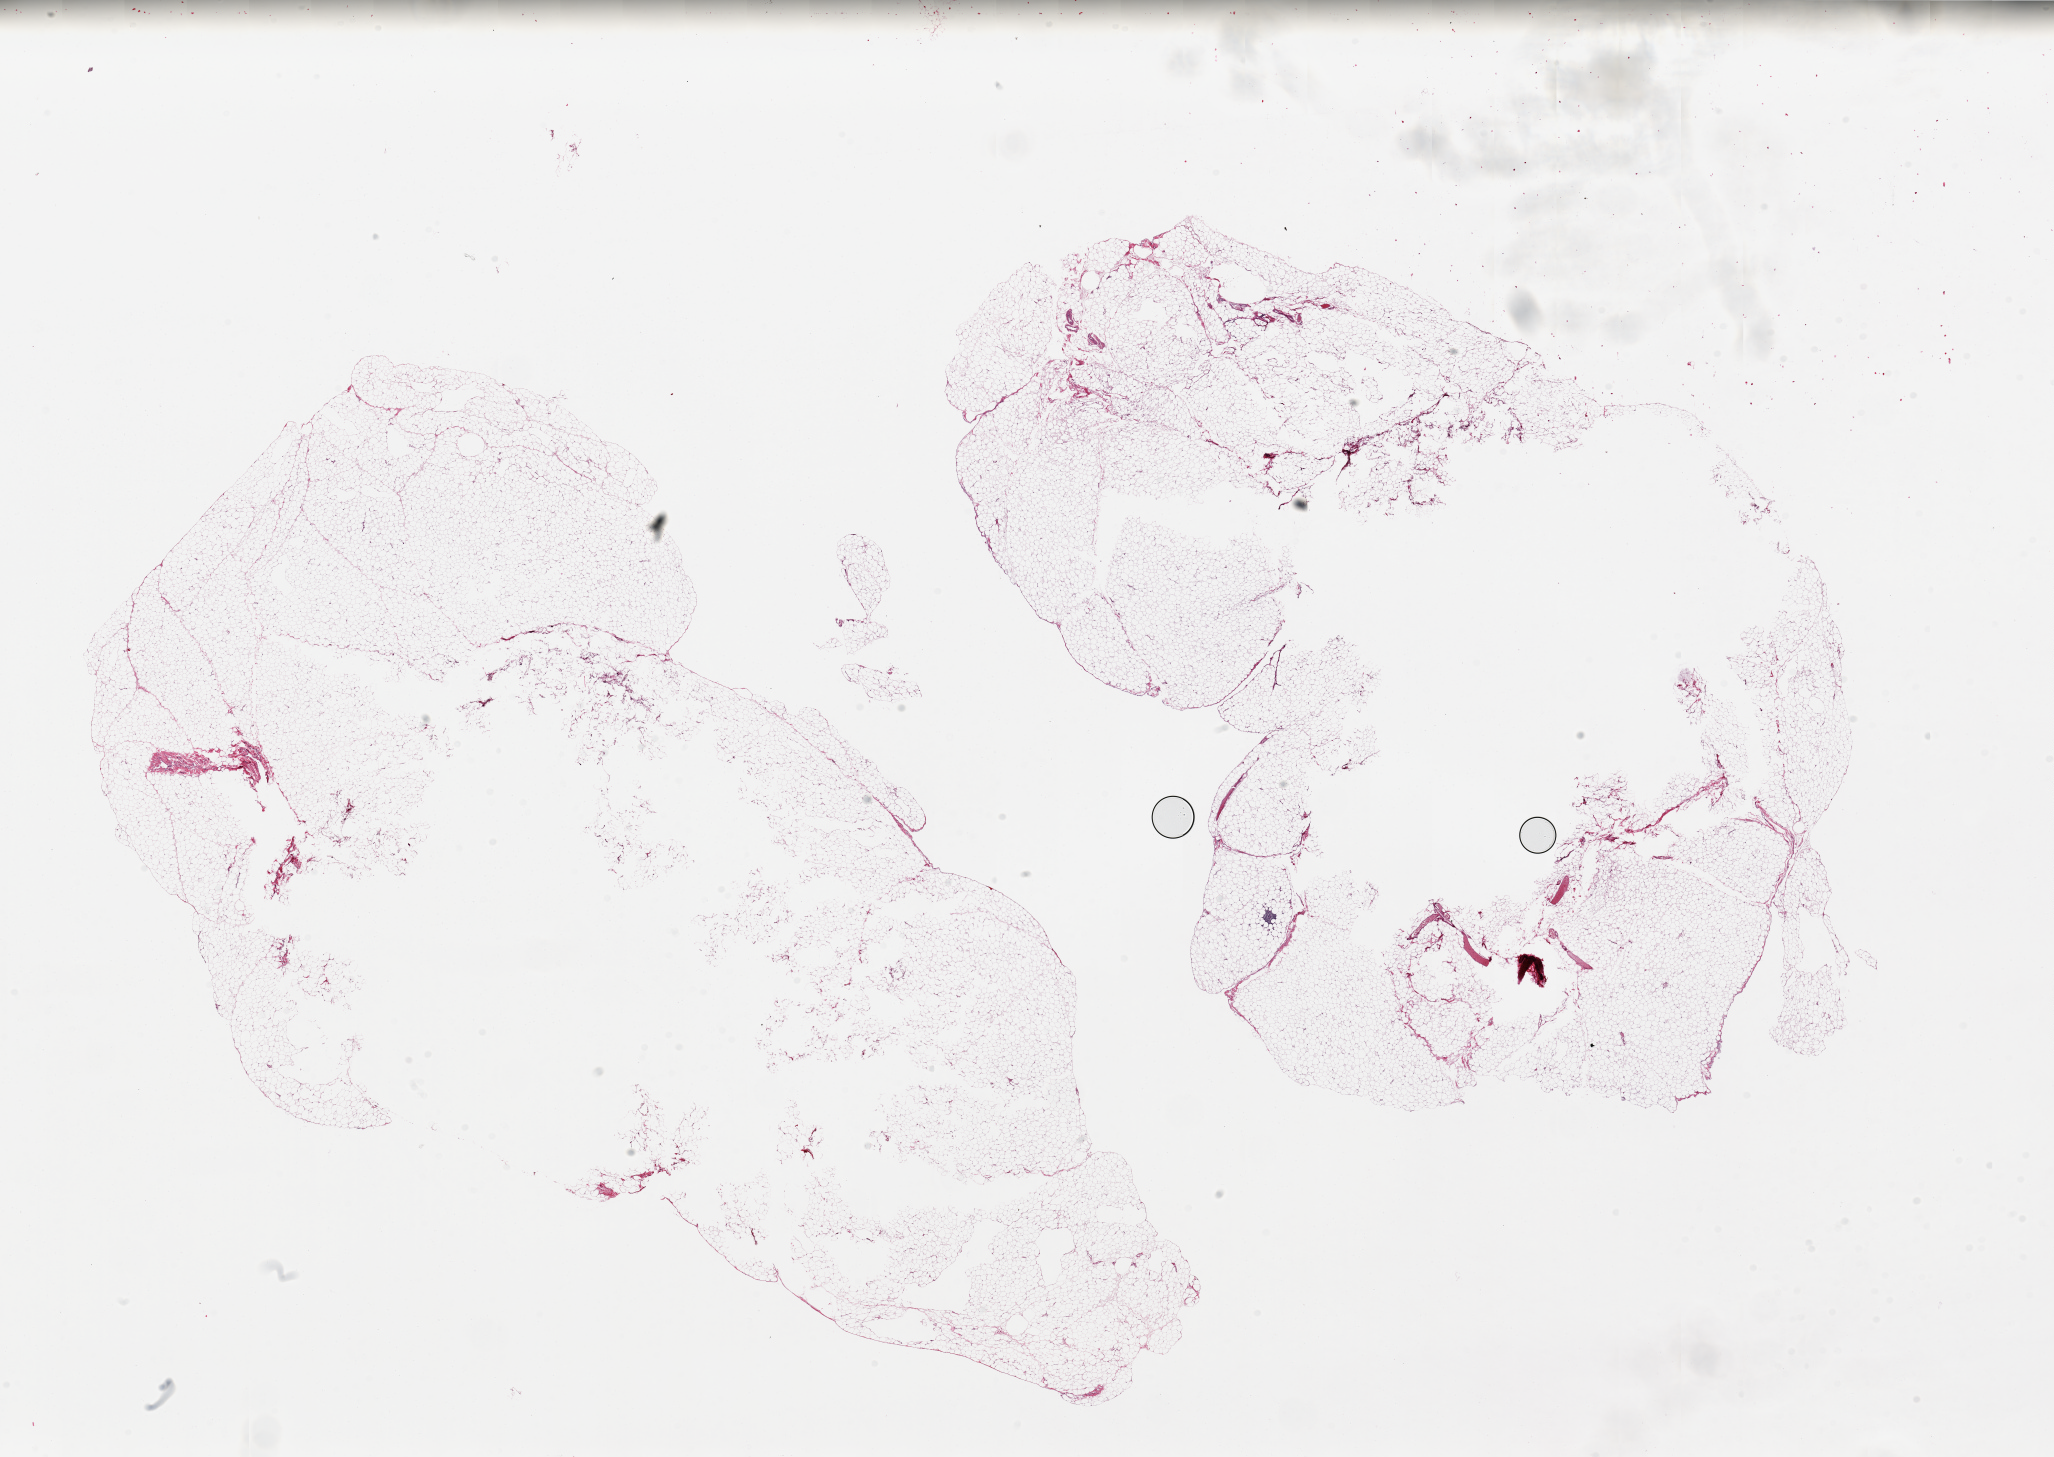
Digitized haematoxylin and eosin-stained section, brightfield — whole scanned area (about 32.5 x 23.0 mm, from a 20x scan) shown as a low-resolution overview, PAXgene-fixed, paraffin-embedded tissue, sampled site (target tissue): omentum, tissue donor sample. Donor: female.
• review note (as recorded): 2 pieces, 20x13 & 18x12mm